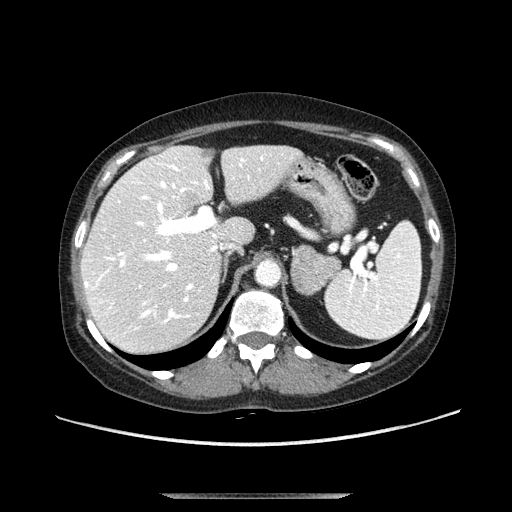
Contrast-enhanced abdominal CT, one axial slice; position 73 of 107 along the scan axis; soft-tissue window (W 400 / L 40 HU); 2.5 mm slice thickness; 512 × 512 image matrix. Female patient. Case-level facts recorded for this patient, not image findings: diagnosis: adrenocortical carcinoma; tumour side: left adrenal; tumour size at pathology: 7.5 cm; Ki-67 index: 9 %; stage (as recorded): 3.
Annotated regions visible in this slice (semi-automatic segmentation, software-assisted and operator-edited):
- mass: box from (x=291, y=244) to (x=342, y=295) px